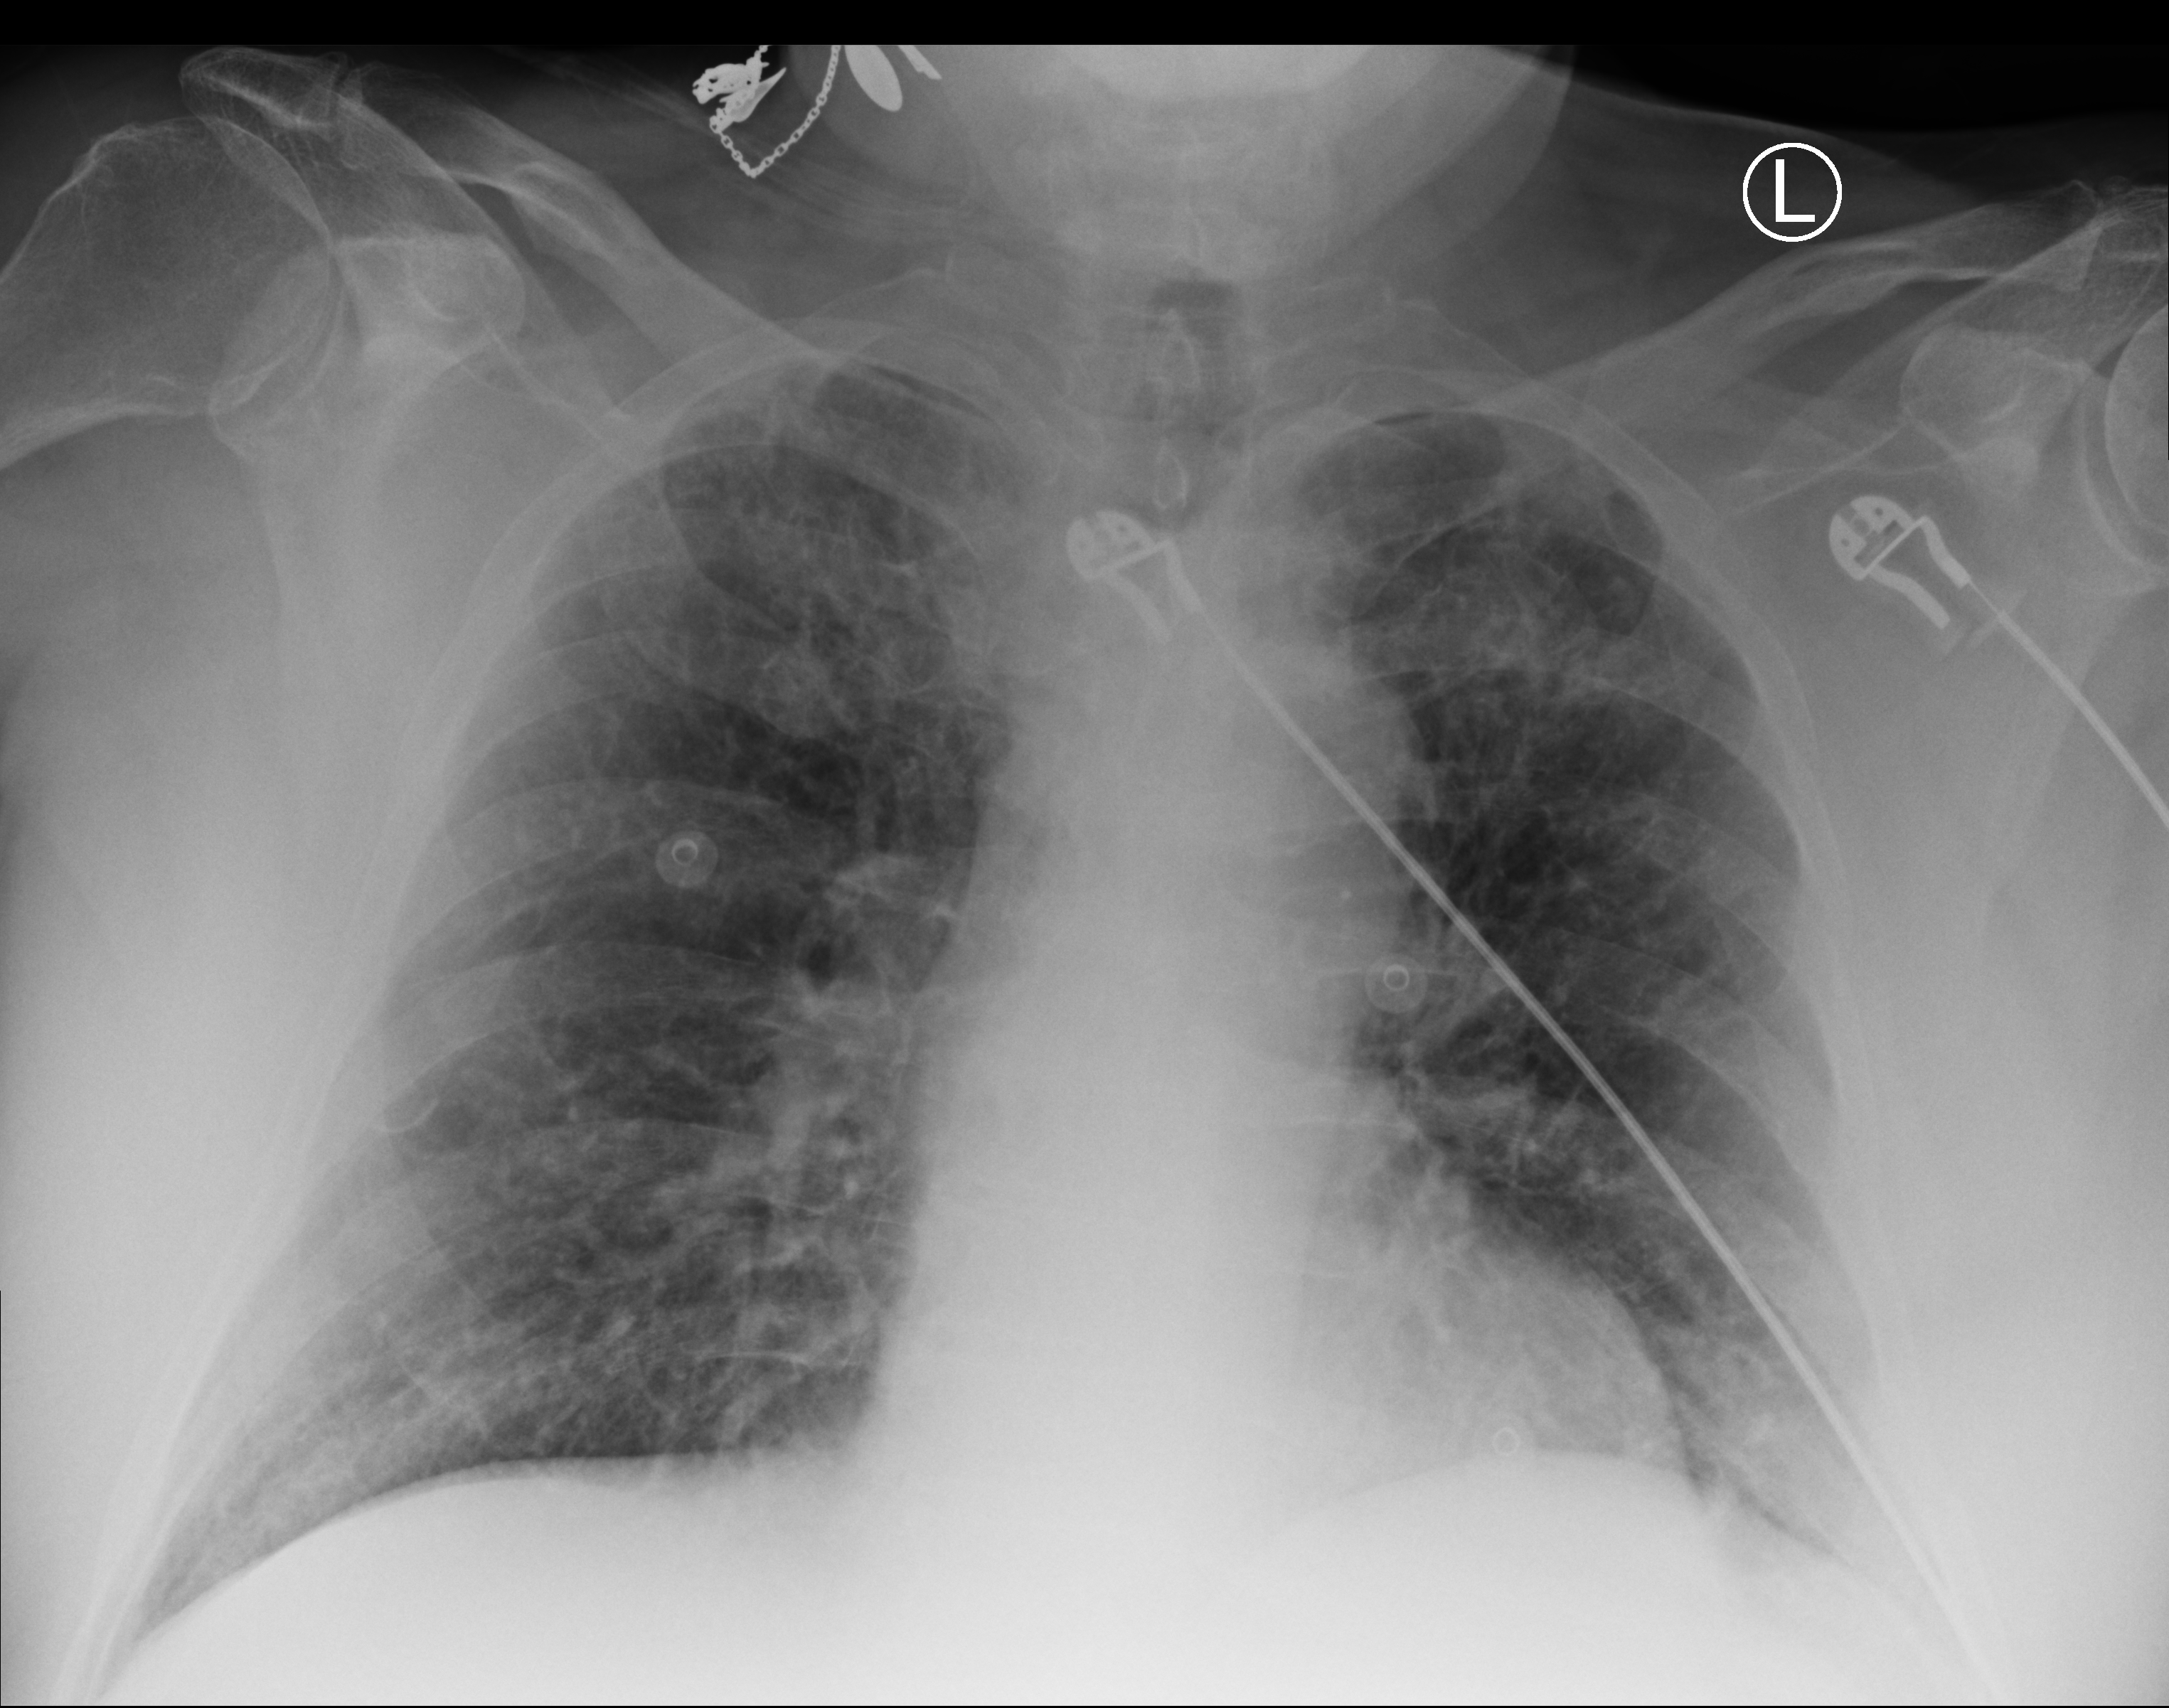
Chest X-ray (portable); anteroposterior (AP) projection. Patient hospitalised with COVID-19; male, aged 75–90 years.
Admission-level facts for this patient (not findings on this image; timing relative to this image not recorded): admitted to intensive care during this hospital stay: no; mechanically ventilated during this hospital stay: no.